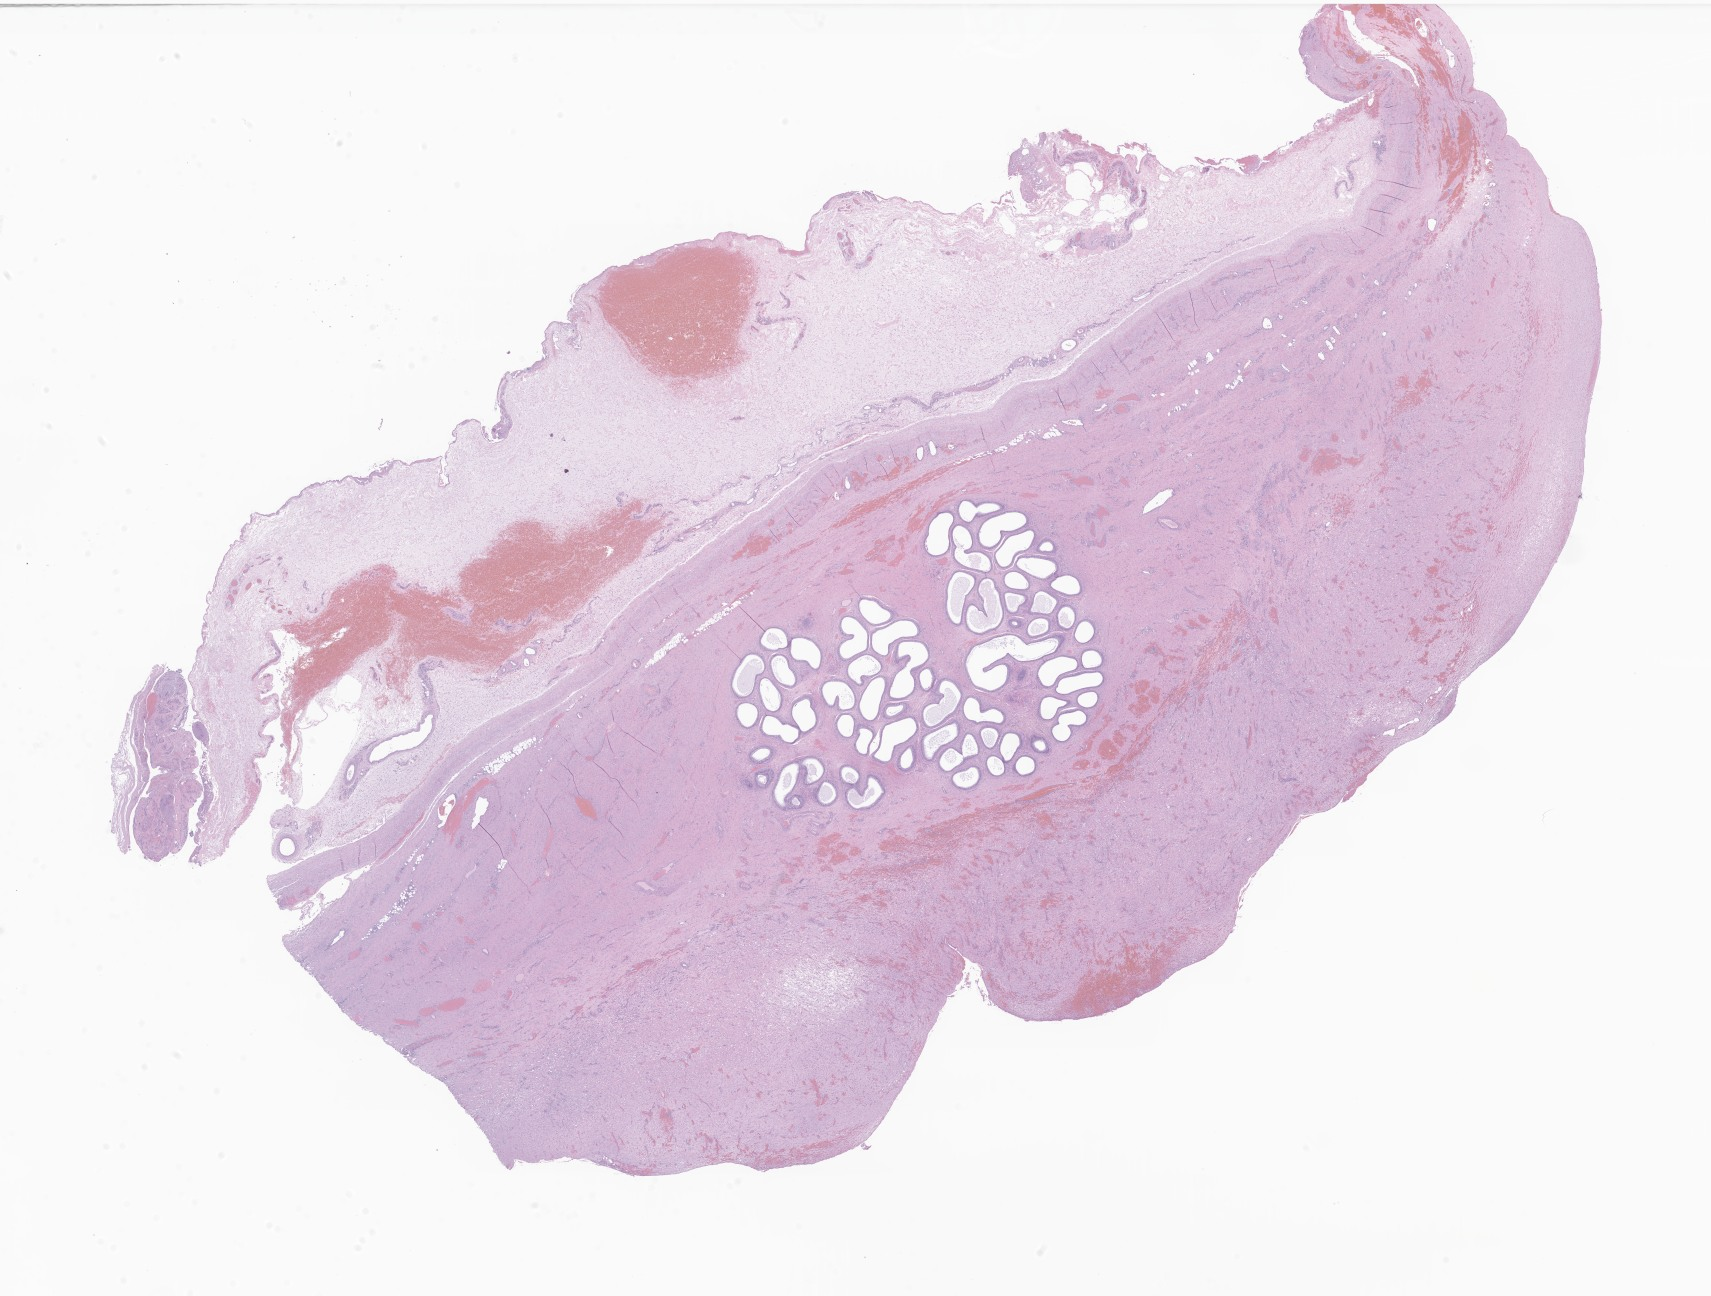
Hematoxylin and eosin (H&E) whole-slide image of tumor tissue from the testis — whole scanned area (about 28.9 x 21.9 mm) shown as a low-resolution overview, formalin-fixed paraffin-embedded section. Patient male; age 237 months (19 years 9 months).
Diagnosis (ICD-O-3 morphology term): Rhabdomyosarcoma, NOS.